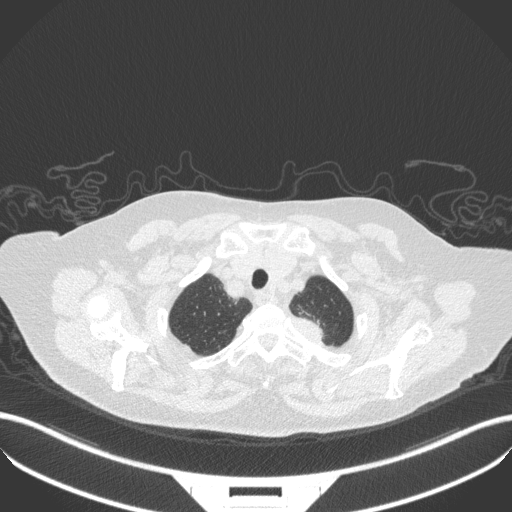
Chest CT, one axial slice; slice 310 of 353 in the series (ordered by position); reconstruction kernel B31f; 100 kVp; lung window (W 1500 / L -600 HU); 1 mm slice thickness; 512 × 512 image matrix. Female patient, age 81 years. Case-level facts recorded for this patient, not image findings: clinical TNM (as recorded): T2a N0 M0.
Structures marked on this image (bounding box drawn by a radiologist):
- lung tumour (recorded histology: adenocarcinoma): bounding box [x1, y1, x2, y2] px = [292, 307, 337, 345]